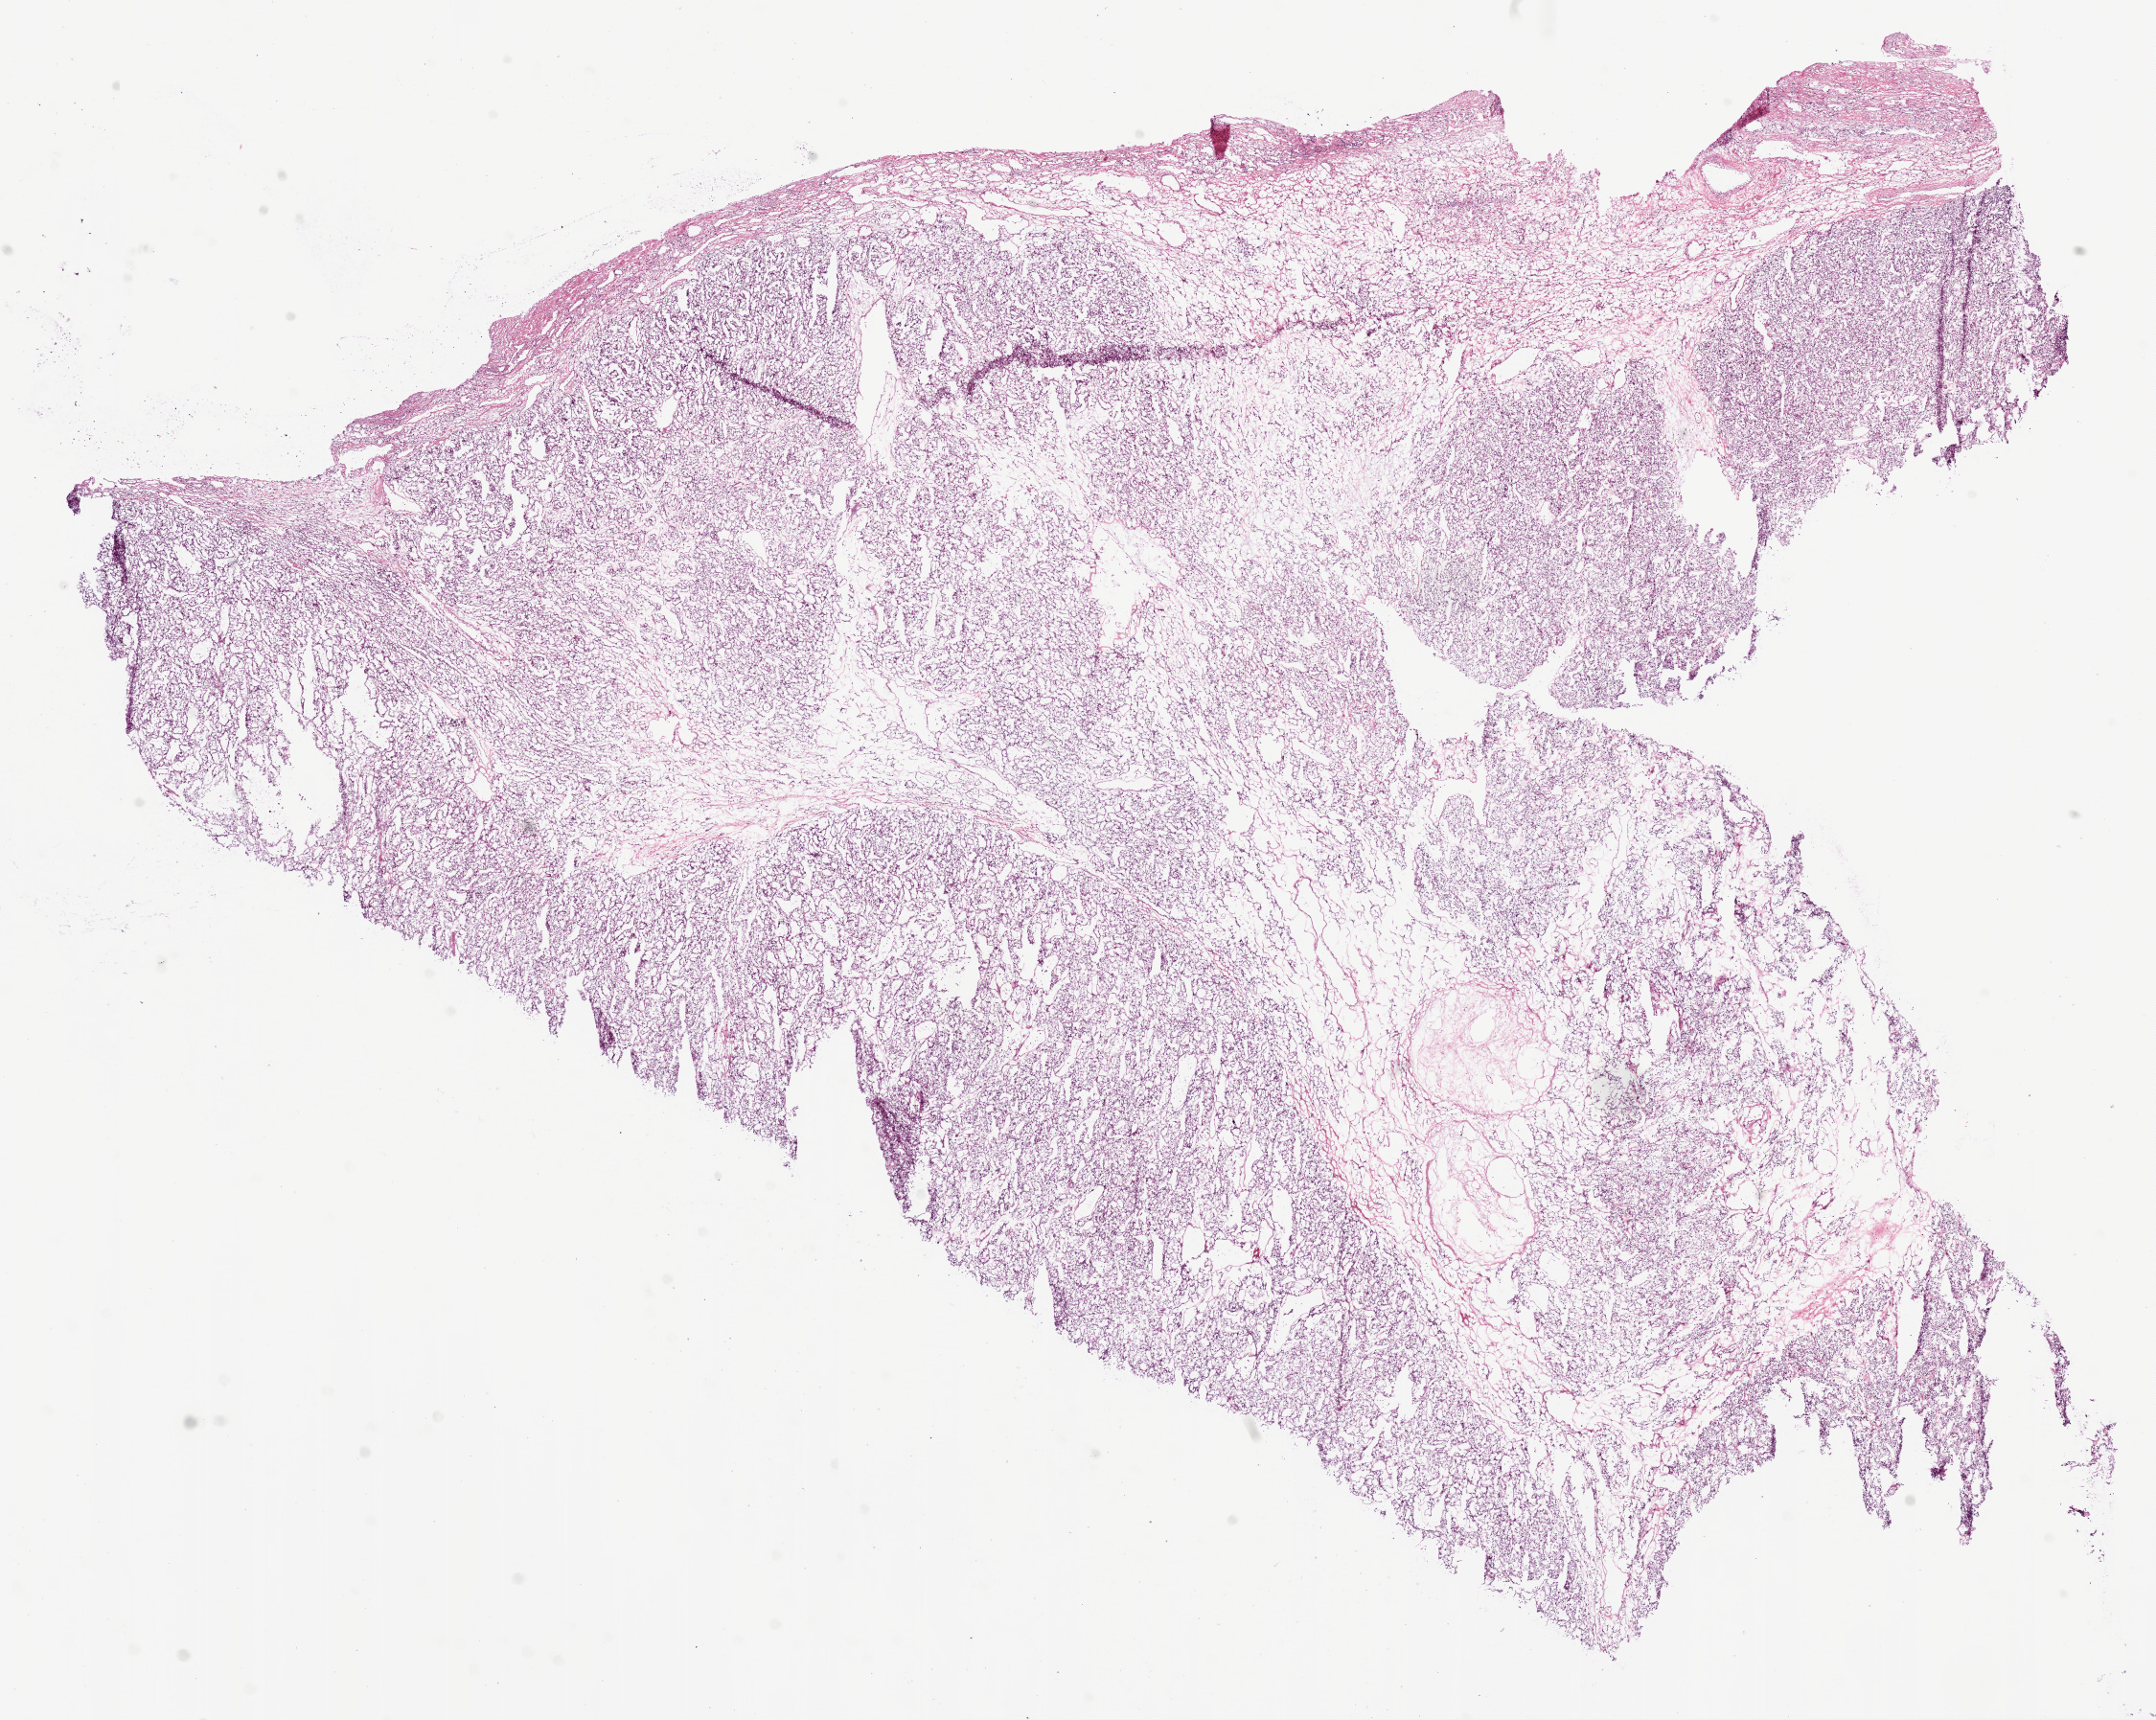
Digitized H&E tissue section (whole slide), low-resolution overview of the scanned area, about 18.1 x 14.4 mm (acquisition: 20x scan). Frozen section. Sample: primary tumour, kidney. Female patient; age at initial diagnosis 80 years. Histologic grade: G2 (moderately differentiated). Slide review estimates, as recorded: tumour cells 90%, tumour nuclei 90%, normal cells 0%, stromal cells 10%, necrosis 0%.
- laterality: left
- AJCC pathologic stage: I
- diagnosis: Clear cell adenocarcinoma, NOS